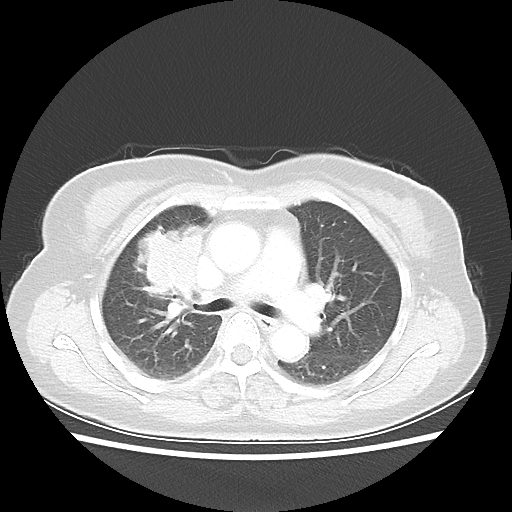
Chest CT, one axial slice; 80 kVp; lung window (W 1500 / L -600 HU); 5 mm slice thickness; 512 × 512 image matrix, field of view 337 × 337 mm. Female patient, age 62 years. From the clinical record (not read from this slice): clinical TNM (as recorded): T4 N3 M0.
Structures marked on this image (bounding box drawn by a radiologist):
- lung tumour (recorded histology: squamous cell carcinoma): box from (x=123, y=215) to (x=210, y=319) px